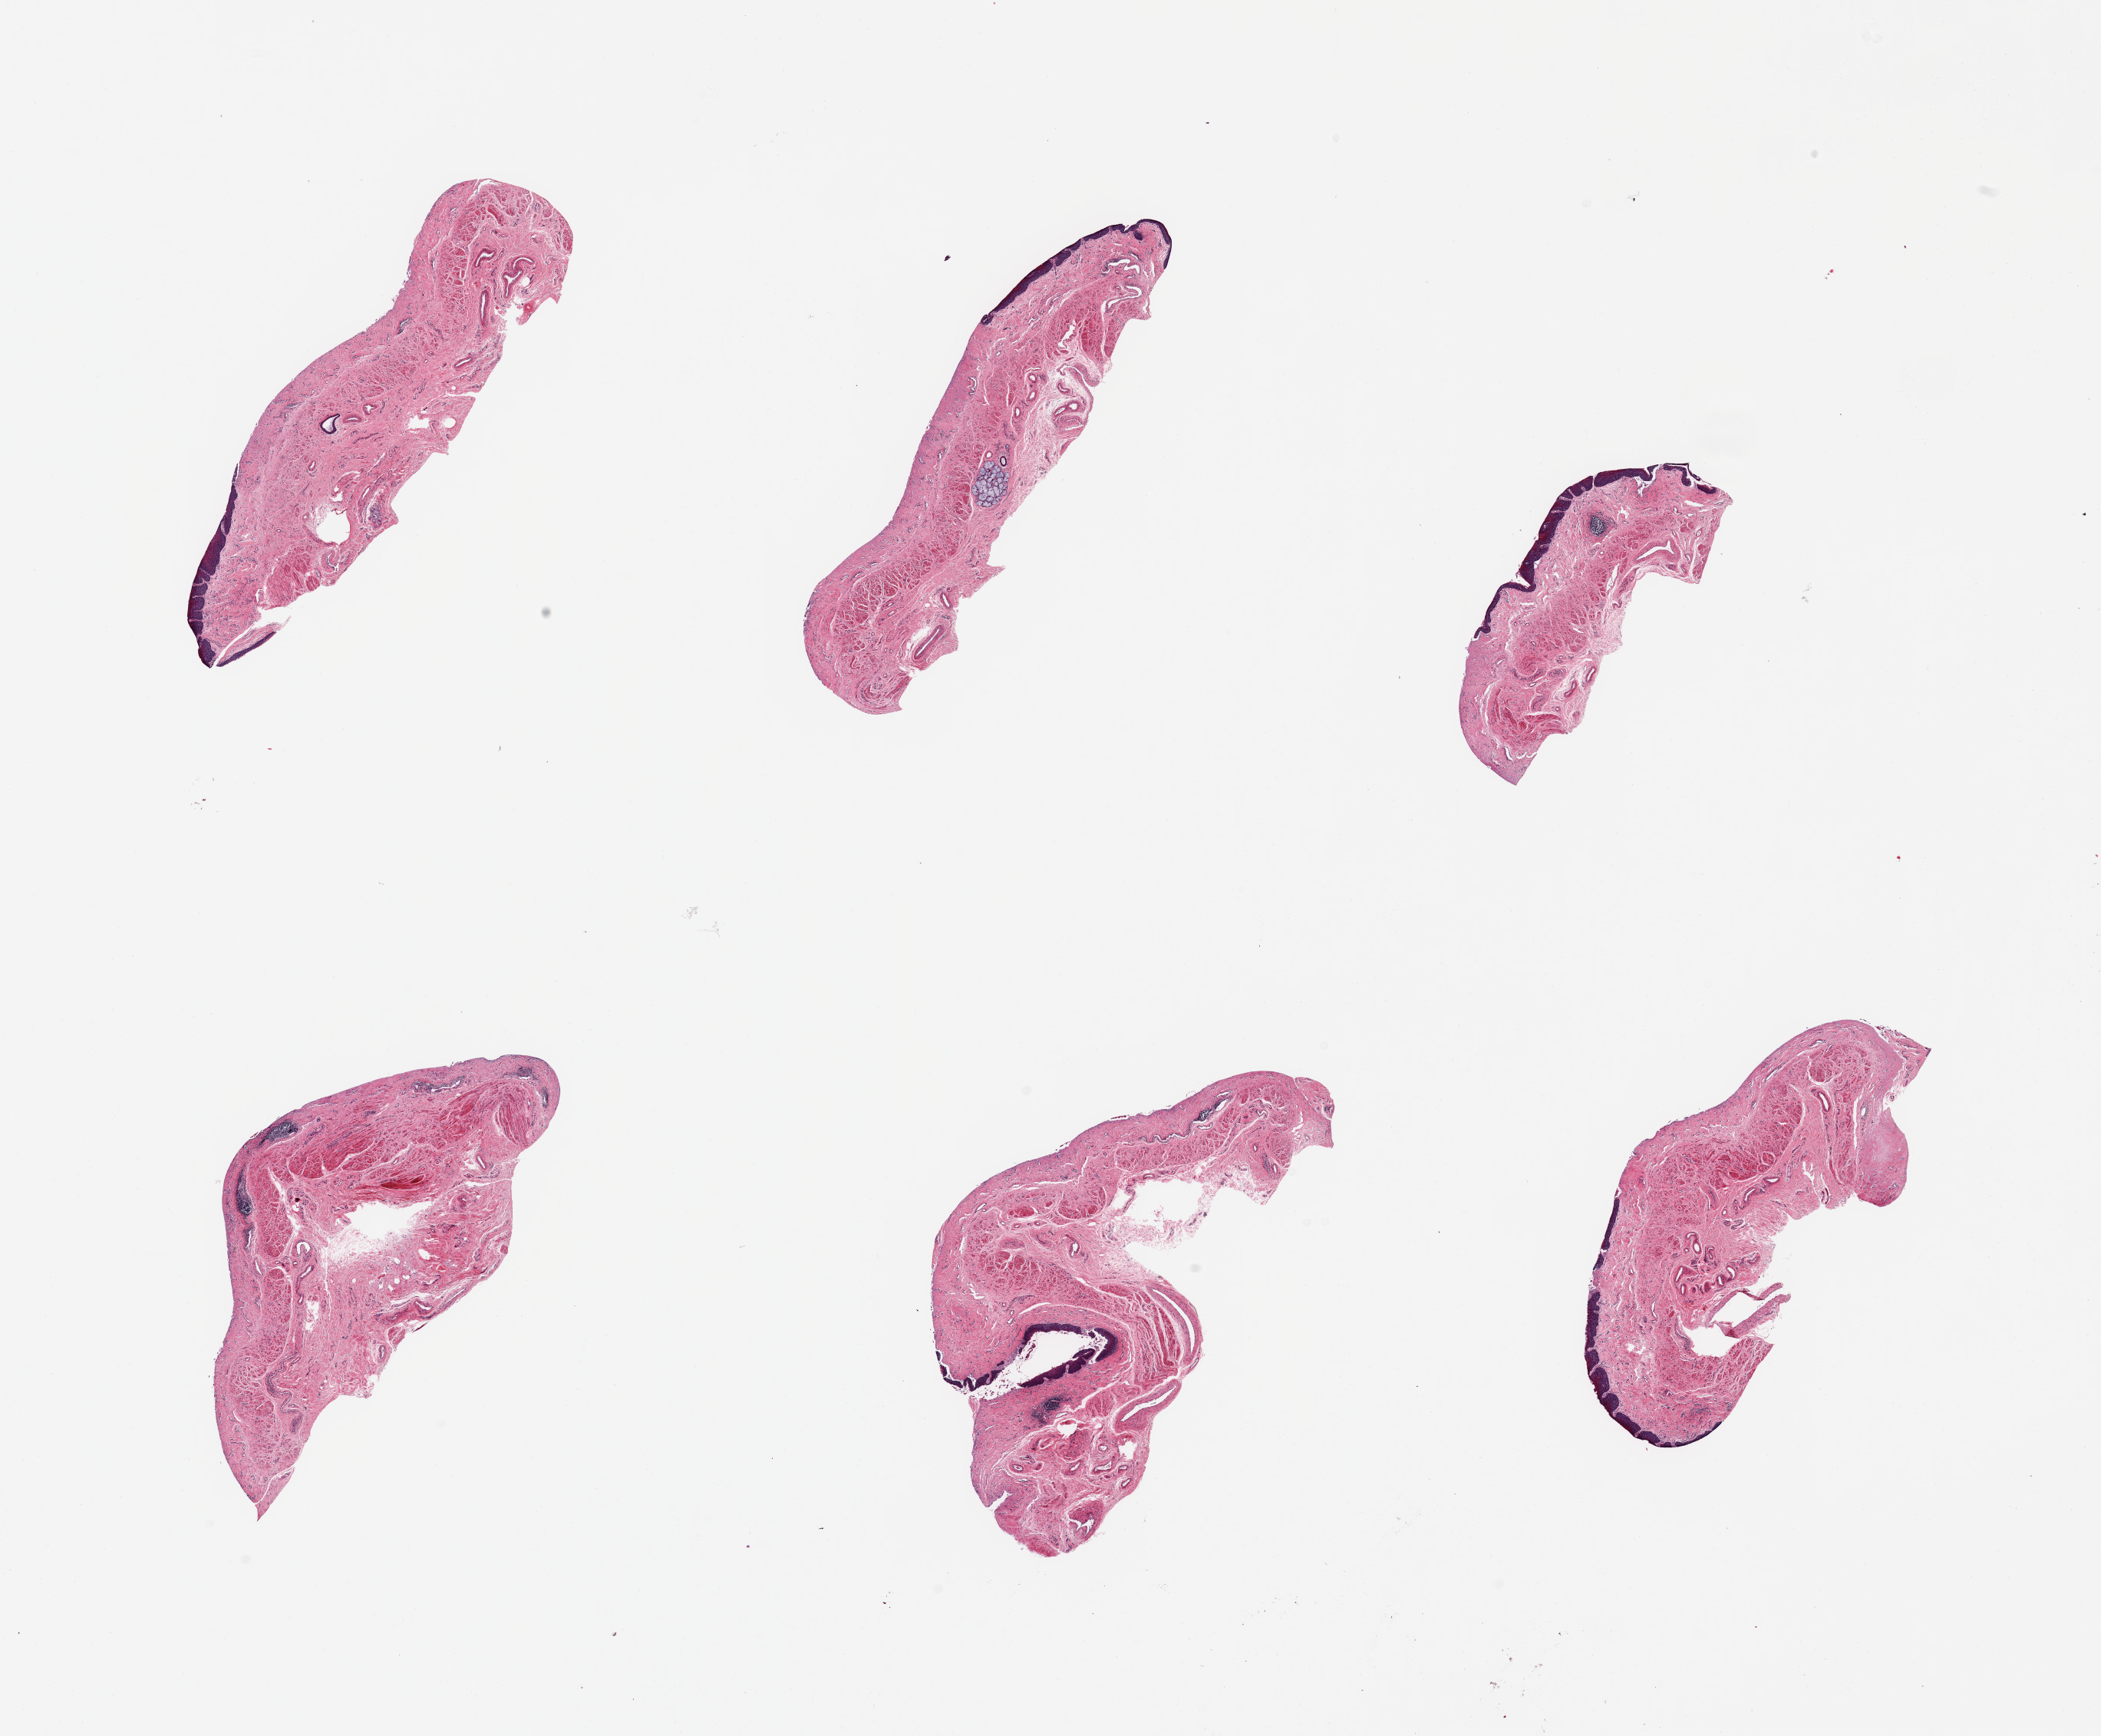
Haematoxylin and eosin whole-slide image, shown as a low-resolution overview of the whole scanned area (about 21.7 x 17.9 mm, acquisition: 20x scan), PAXgene-fixed, paraffin-embedded tissue, target tissue: esophageal mucous membrane, tissue donor sample. Donor: male.
Review note (as recorded): 6 pieces; largely sloughed squamous surface.